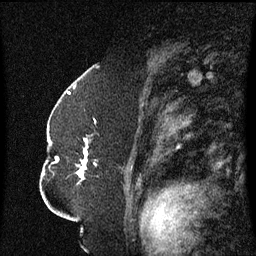
Breast MRI (dynamic contrast-enhanced), one sagittal slice. Slice 41 of 60 in the series (ordered by position). Dynamic contrast-enhanced series, image 2 of 3 at this slice position (ordered by acquisition). 1.5 T. TE 4.2 ms, TR 8.4 ms. 2.3 mm slice thickness. 256 × 256 image matrix. Female patient, age 52 years. Case-level facts recorded for this patient, not image findings: setting: breast cancer imaged before/during neoadjuvant chemotherapy; receptor status: HR-positive, HER2-negative.
Outlined on this slice (semi-automatic segmentation, software-assisted and operator-edited):
- analysis volume of interest (the breast-tissue region the enhancement analysis was run in; not a lesion): bounding box [x1, y1, x2, y2] px = [49, 124, 97, 185]
- tumour enhancement mask (voxels above the 70 % enhancement threshold inside the analysis volume of interest): [56, 140, 88, 181]